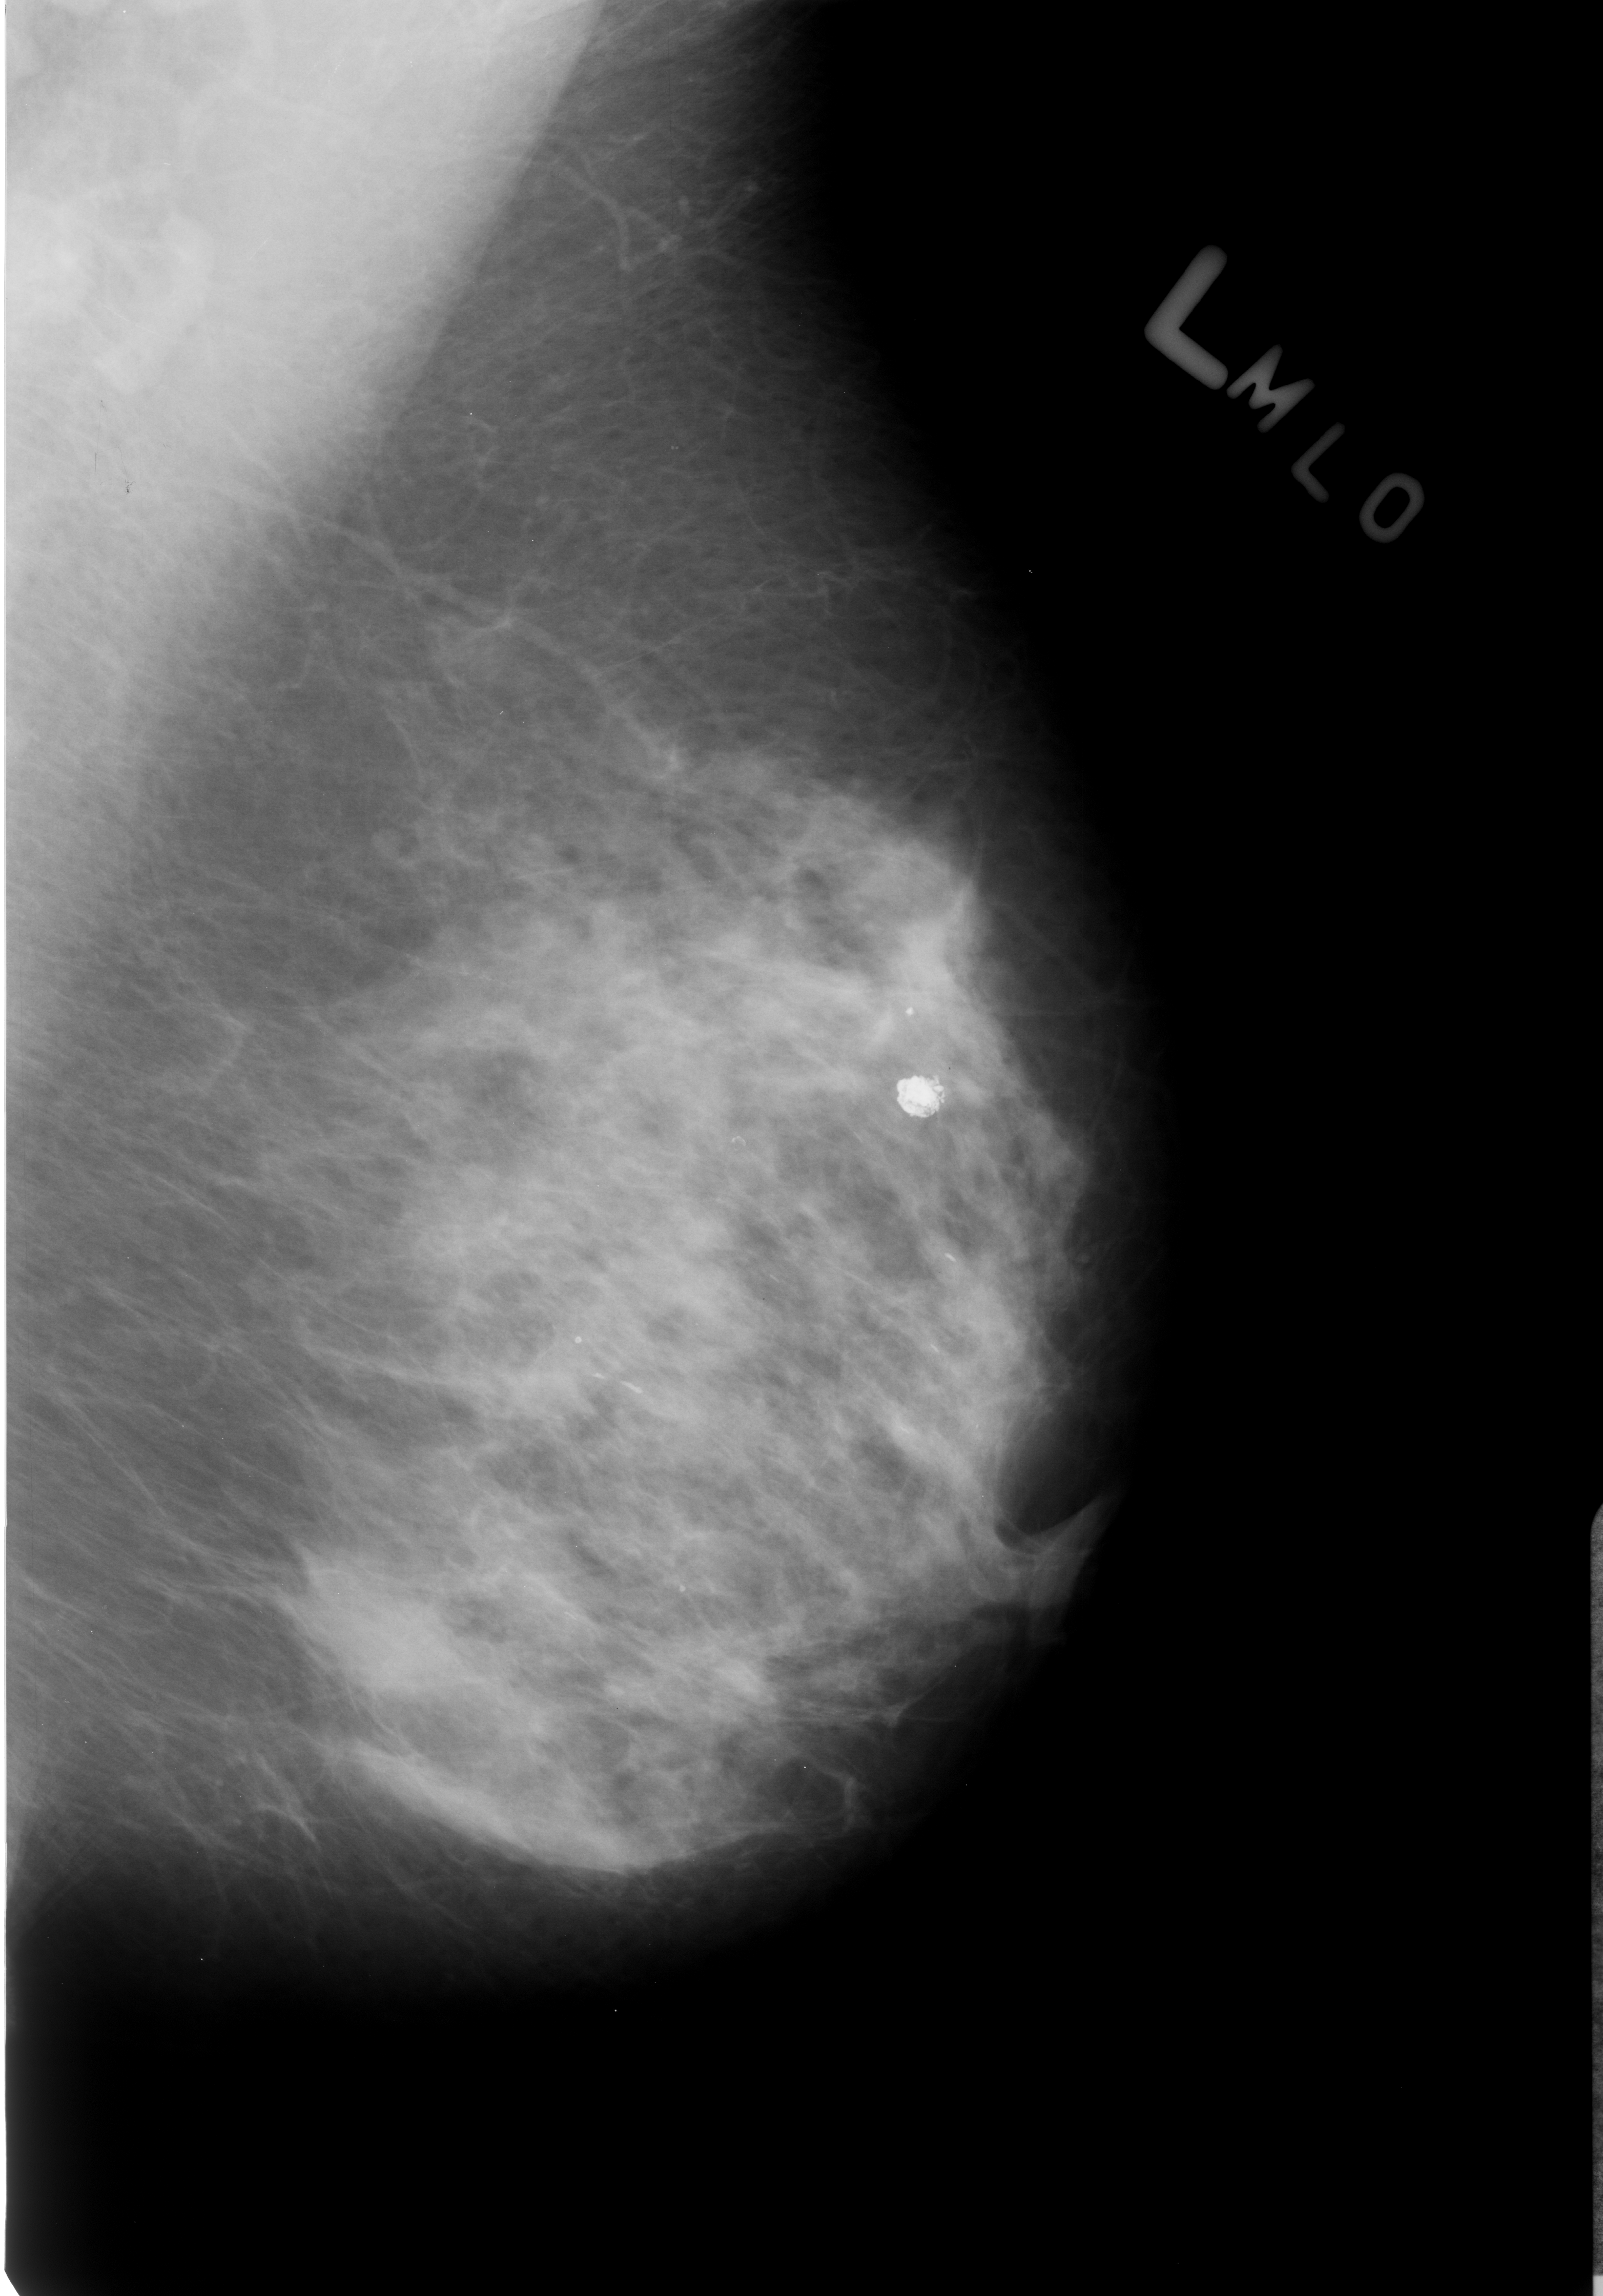
Mammogram (digitized film); left breast; mediolateral oblique (MLO) view; breast composition: heterogeneously dense (BI-RADS density category 3 of 4); 1603 × 2296 image matrix.
Expert-marked regions of interest on this film, with their recorded descriptors:
- calcifications, distribution linear; BI-RADS assessment category 2; outcome (as recorded, no biopsy): benign without callback (not worked up further): bounding box [x1, y1, x2, y2] px = [889, 1074, 948, 1120]